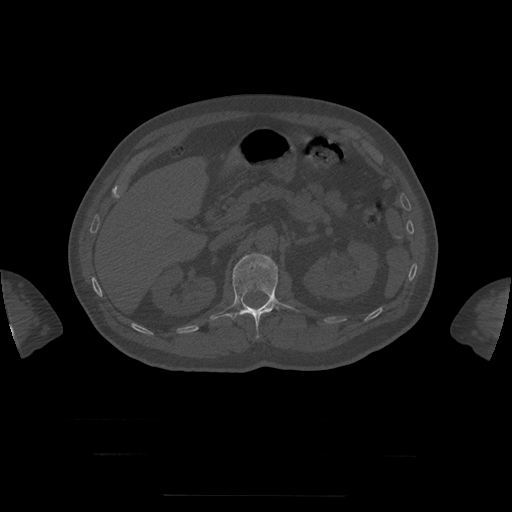
CT including the spine, one axial slice; slice 49 of 397 in the series (ordered by position); bone window (W 1800 / L 400 HU); 1.25 mm slice thickness; 512 × 512 image matrix. Patient age 73 years. Case-level facts recorded for this patient, not image findings: primary cancer: prostate.
Structures marked on this image (semi-automatically segmented with operator editing):
- L1 vertebra: bounding box [x1, y1, x2, y2] px = [211, 254, 299, 338]
- T8 vertebra: [236, 313, 242, 316]